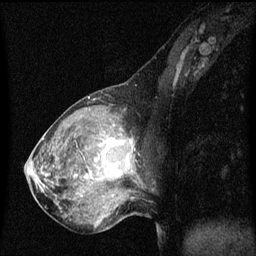
Breast MRI (dynamic contrast-enhanced), one sagittal slice; slice 25 of 60 in the series (ordered by position); dynamic contrast-enhanced series, image 2 of 3 at this slice position (ordered by acquisition); 1.5 T; TE 4.2 ms, TR 8 ms; 2 mm slice thickness; 256 × 256 image matrix, field of view 200 × 200 mm. Female patient, age 50 years.
Outlined on this slice (semi-automatic segmentation, software-assisted and operator-edited):
- analysis volume of interest (the breast-tissue region the enhancement analysis was run in; not a lesion): bounding box [x1, y1, x2, y2] px = [91, 126, 141, 189]
- tumour enhancement mask (voxels above the 70 % enhancement threshold inside the analysis volume of interest): [91, 138, 132, 181]